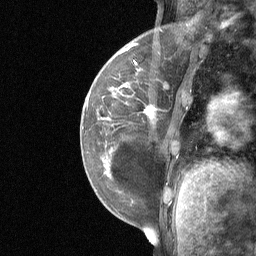
Breast MRI (dynamic contrast-enhanced), one sagittal slice; position 17 of 64 along the scan axis; dynamic contrast-enhanced study with each time point stored as its own series, time point 2 of 3 at this slice position (early post-contrast, ordered by acquisition time); 1.5 T; TE 4.8 ms, TR 27 ms; 2 mm slice thickness; 256 × 256 image matrix, field of view 200 × 200 mm. Female patient, age 34 years. From the clinical record (not read from this slice): setting: breast cancer imaged before/during neoadjuvant chemotherapy; receptor status: HR-positive, HER2-negative.
Annotated regions visible in this slice (semi-automatically segmented with operator editing):
- analysis volume of interest (the breast-tissue region the enhancement analysis was run in; not a lesion): bounding box (x1, y1, x2, y2) in pixels: (92, 50, 188, 185)
- tumour enhancement mask (voxels above the 90 % enhancement threshold inside the analysis volume of interest): (136, 63, 151, 116)